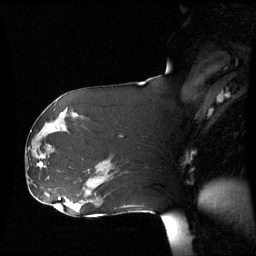
Breast MRI (dynamic contrast-enhanced), one sagittal slice. Position 31 of 60 along the scan axis. Dynamic contrast-enhanced series, image 2 of 3 at this slice position (ordered by acquisition). 1.5 T. TE 4.2 ms, TR 8.9 ms. 2.7 mm slice thickness. 256 × 256 image matrix, field of view 280 × 280 mm. Patient: female, 61 years. Case-level facts recorded for this patient, not image findings: setting: breast cancer imaged before/during neoadjuvant chemotherapy; receptor status: HR-positive, HER2-negative.
Outlined on this slice (semi-automatic segmentation, software-assisted and operator-edited):
- analysis volume of interest (the breast-tissue region the enhancement analysis was run in; not a lesion): bounding box (x1, y1, x2, y2) in pixels: (26, 142, 55, 169)
- tumour enhancement mask (voxels above the 70 % enhancement threshold inside the analysis volume of interest): (38, 158, 45, 167)